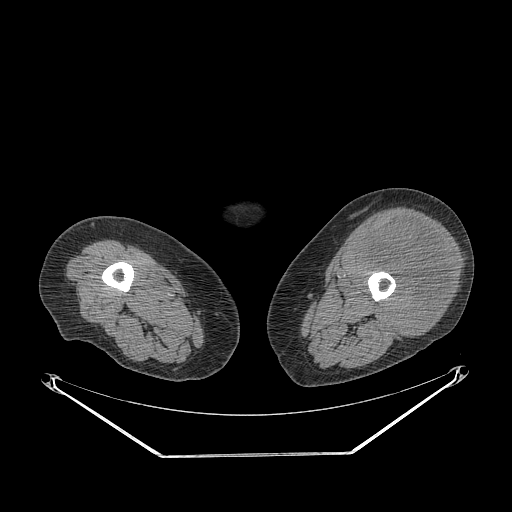
CT of an extremity soft-tissue mass (from a PET/CT study), one axial slice. Slice 220 of 267 in the series (ordered by position). Reconstruction kernel STANDARD. 140 kVp. Soft-tissue window (W 400 / L 40 HU). 3.75 mm slice thickness. 512 × 512 image matrix, field of view 500 × 500 mm. Female patient. From the clinical record (not read from this slice): histological type: undifferentiated – high grade; grade: high; site of the primary tumour: left thigh.
Structures marked on this image (expert contour drawn on MRI and transferred to this co-registered scan by the dataset authors):
- gross tumour volume including surrounding oedema: bounding box <358,217,453,336> (left, top, right, bottom; pixels)
- gross tumour volume (mass): <358,217,453,336>